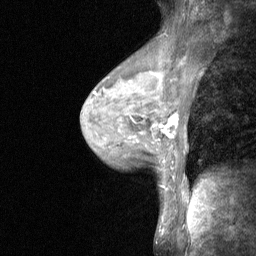
Breast MRI (dynamic contrast-enhanced), one sagittal slice. Position 38 of 64 along the scan axis. Dynamic contrast-enhanced study with each time point stored as its own series, time point 2 of 3 at this slice position (early post-contrast, ordered by acquisition time). 1.5 T. TE 4.8 ms, TR 27 ms. 256 × 256 image matrix, field of view 200 × 200 mm. Female patient, age 44 years. From the clinical record (not read from this slice): setting: breast cancer imaged before/during neoadjuvant chemotherapy; receptor status: HR-positive, HER2-negative.
Annotated regions visible in this slice (semi-automatically segmented with operator editing):
- analysis volume of interest (the breast-tissue region the enhancement analysis was run in; not a lesion): bounding box [x1, y1, x2, y2] px = [140, 109, 180, 148]
- tumour enhancement mask (voxels above the 90 % enhancement threshold inside the analysis volume of interest): [160, 114, 178, 137]